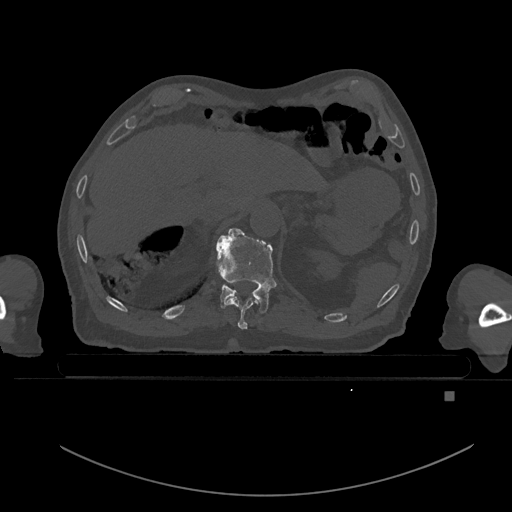
CT including the spine, one axial slice; position 52 of 969 along the scan axis; bone window (W 1800 / L 400 HU); 0.5 mm slice thickness; 512 × 512 image matrix. Male patient, age 82 years. Case-level facts recorded for this patient, not image findings: primary cancer: prostate; vertebrae with lytic lesions (as recorded): T11, T9, T8, T2.
Annotated regions visible in this slice (semi-automatic segmentation, software-assisted and operator-edited):
- T10 vertebra: box from (x=226, y=296) to (x=259, y=330) px
- T11 vertebra: (x=216, y=228)–(x=276, y=313)